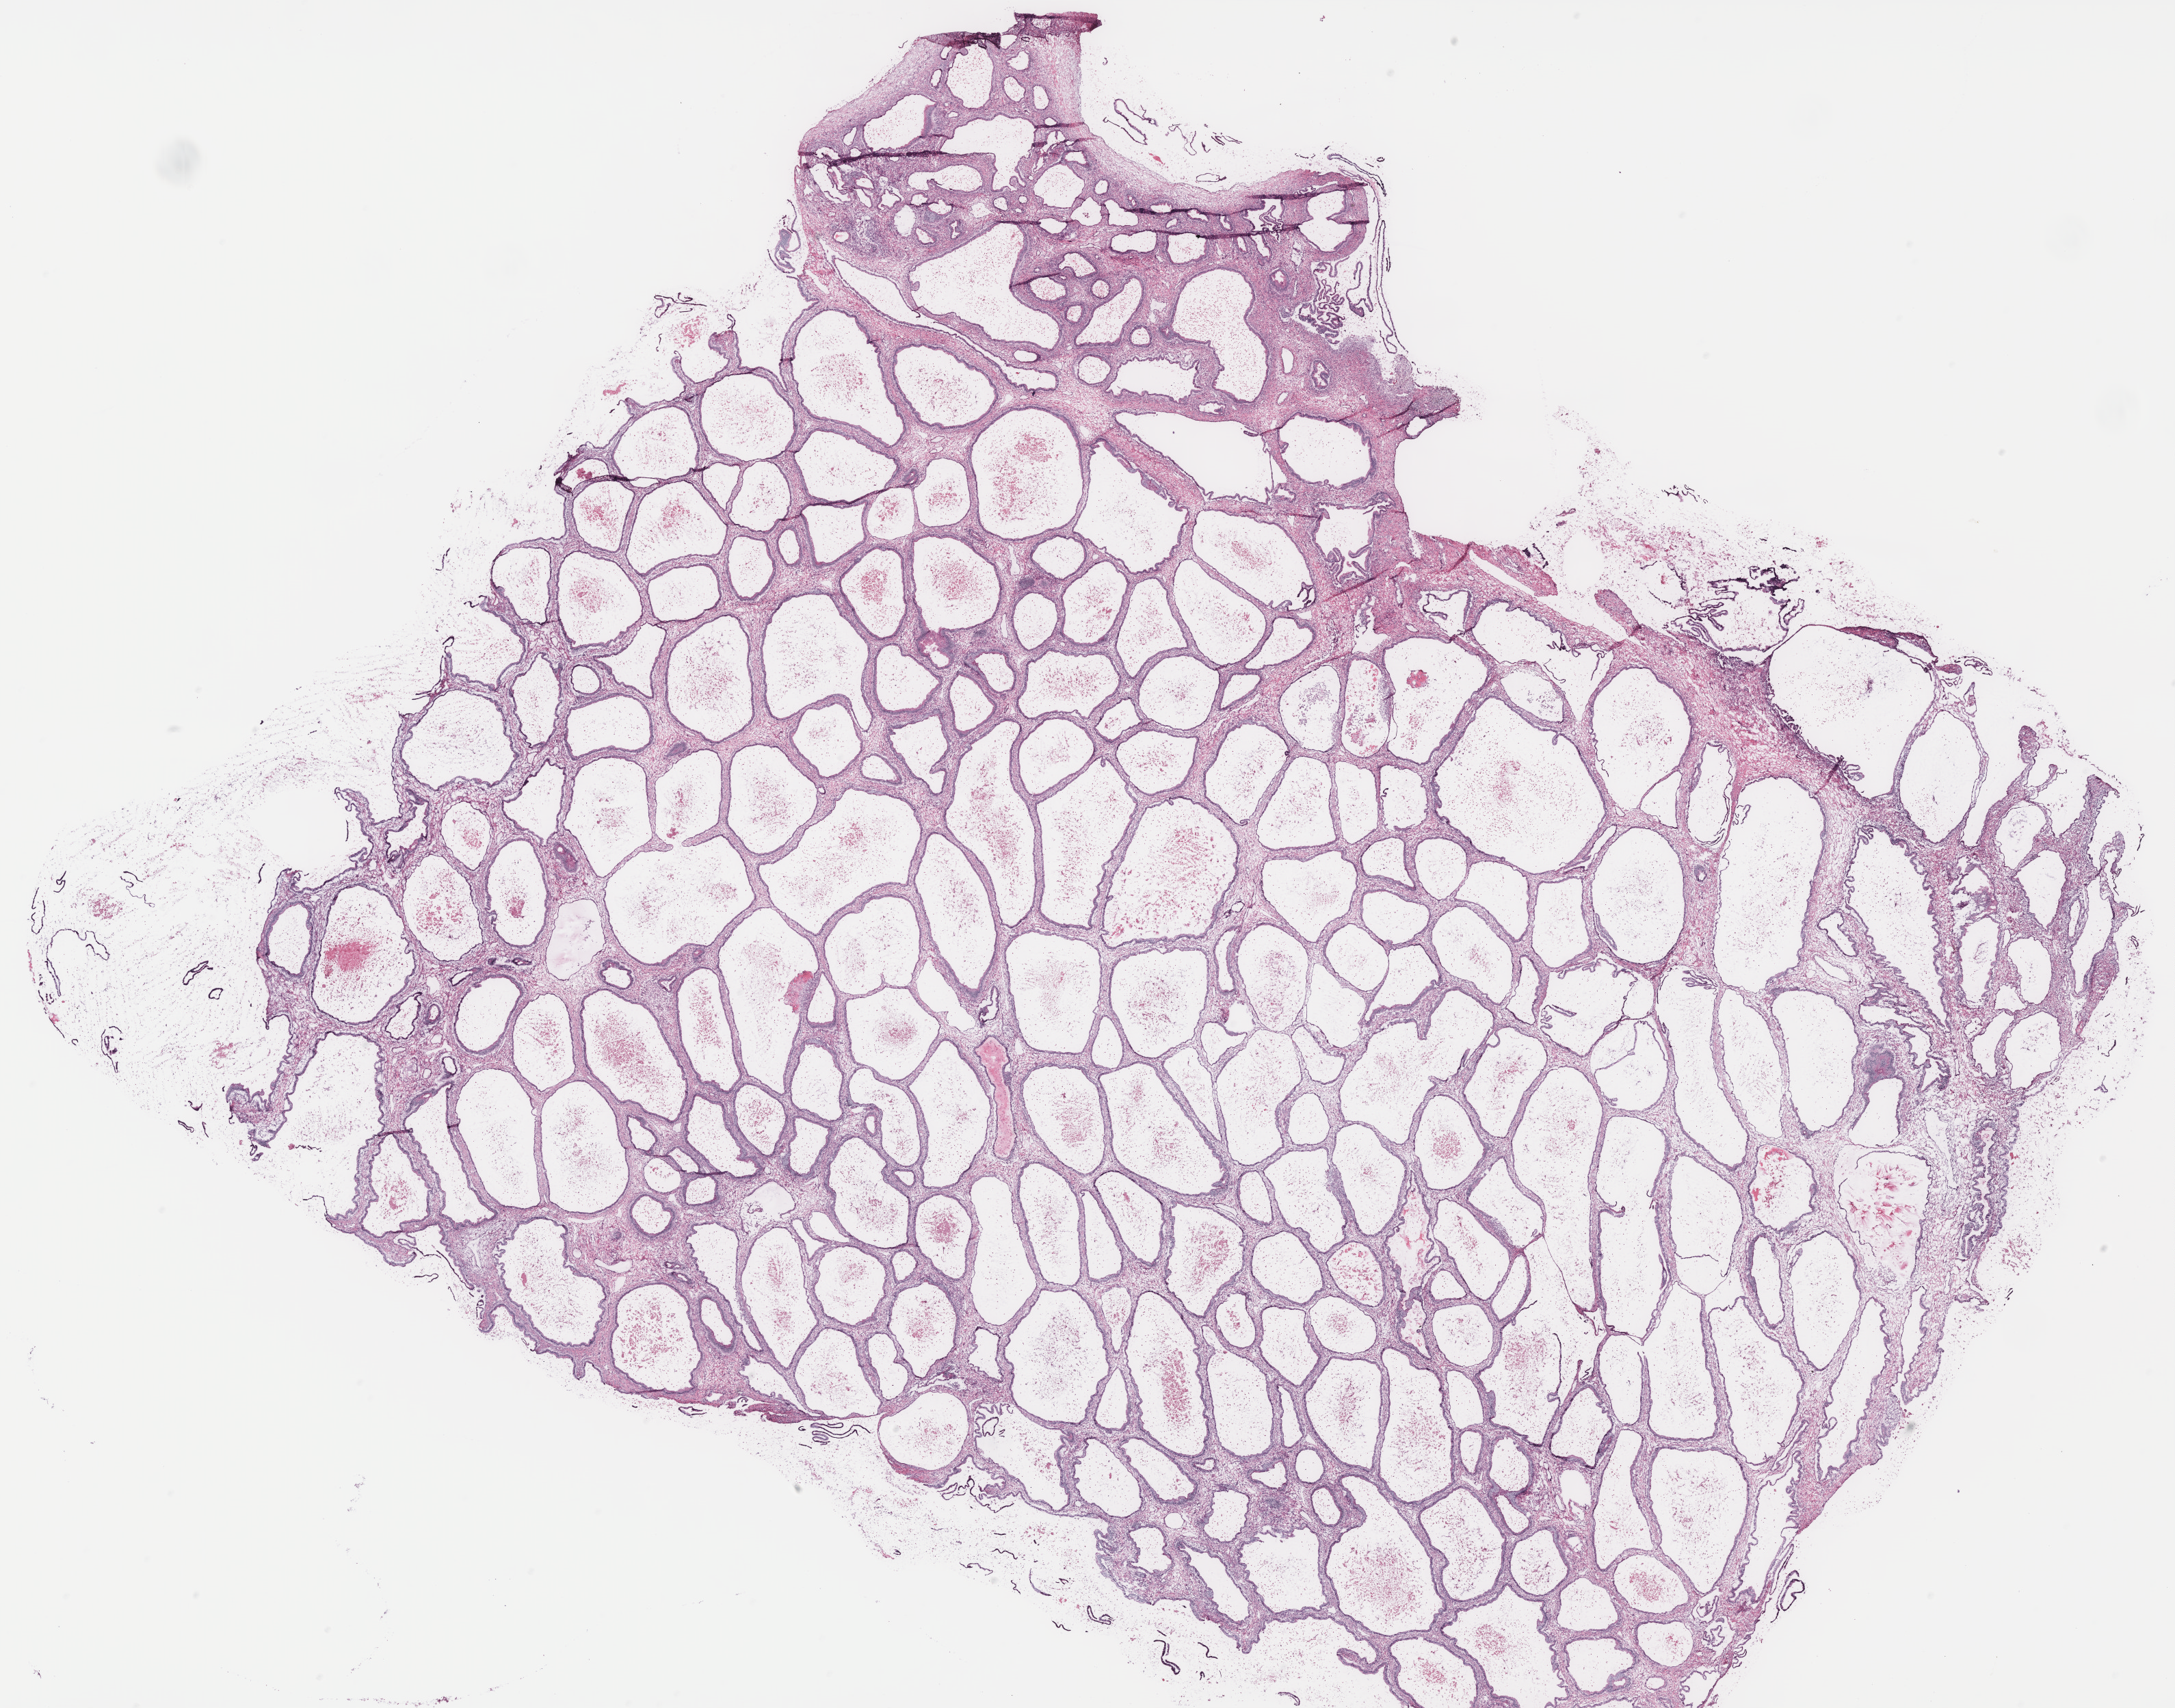
Digitized H&E-stained tissue section (whole slide) — shown as a low-resolution overview of the whole scanned area (about 25.5 x 20.0 mm), ovary, tumour tissue. Female, 52 y/o.
- patient diagnosis (cohort enrolment): ovarian cancer (ovary)